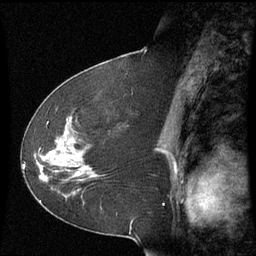
Breast MRI (dynamic contrast-enhanced), one sagittal slice; slice 32 of 60 in the series (ordered by position); dynamic contrast-enhanced series, image 2 of 3 at this slice position (ordered by acquisition); 1.5 T; TE 4.2 ms, TR 8.9 ms; 2.3 mm slice thickness; 256 × 256 image matrix. Patient: female, 51 years. Case-level facts recorded for this patient, not image findings: setting: breast cancer imaged before/during neoadjuvant chemotherapy; receptor status: HR-positive, HER2-negative.
Structures marked on this image (semi-automatic segmentation, software-assisted and operator-edited):
- analysis volume of interest (the breast-tissue region the enhancement analysis was run in; not a lesion): bounding box <50,119,100,184> (left, top, right, bottom; pixels)
- tumour enhancement mask (voxels above the 70 % enhancement threshold inside the analysis volume of interest): <65,133,80,175>